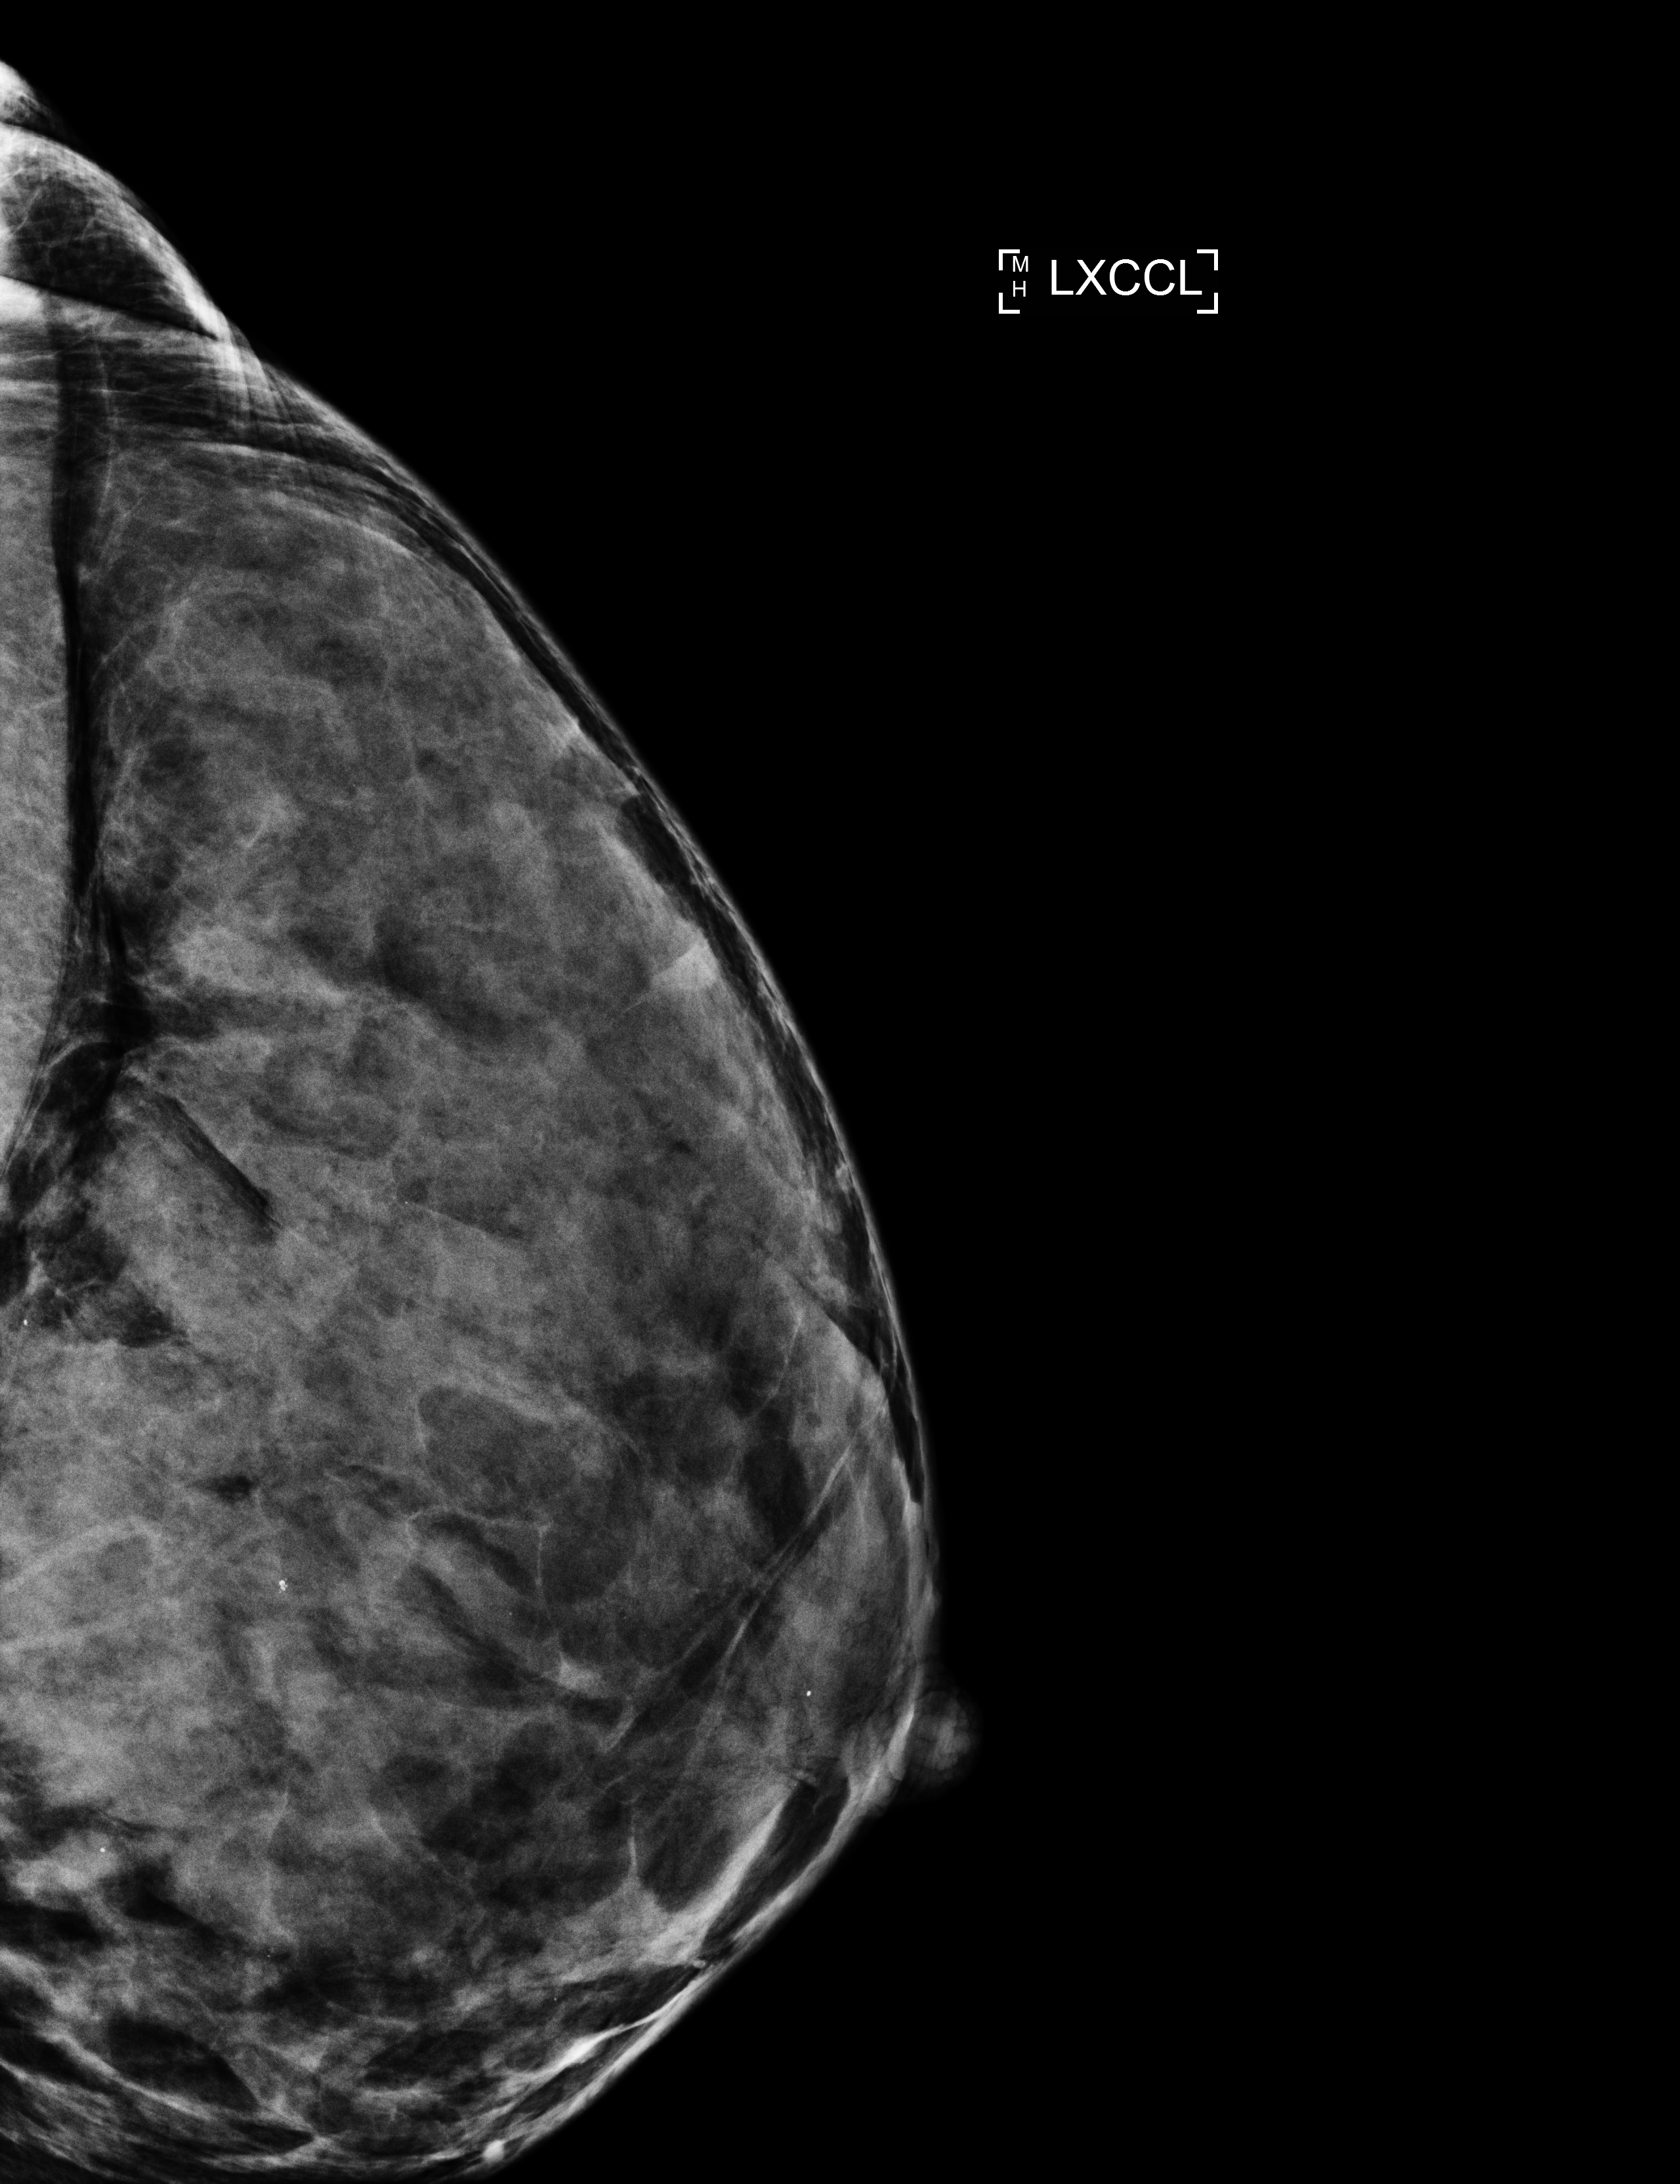
Screening examination. Female patient, age 42 years.
Image type: full-field digital mammogram. Breast: left. Projection: laterally exaggerated craniocaudal (XCCL) view.